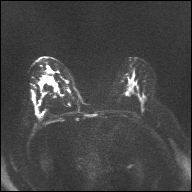
Breast MRI, one axial slice. Slice 19 of 32 in the series (ordered by position). Diffusion-weighted series; image 2 of 4 stored at this slice position (different b-values; order by instance number). 1.5 T. 4 mm slice thickness. 192 × 192 image matrix. Female patient.
Outlined on this slice (outlined manually by an expert reader):
- tumour on diffusion-weighted imaging: box from (x=46, y=70) to (x=50, y=74) px